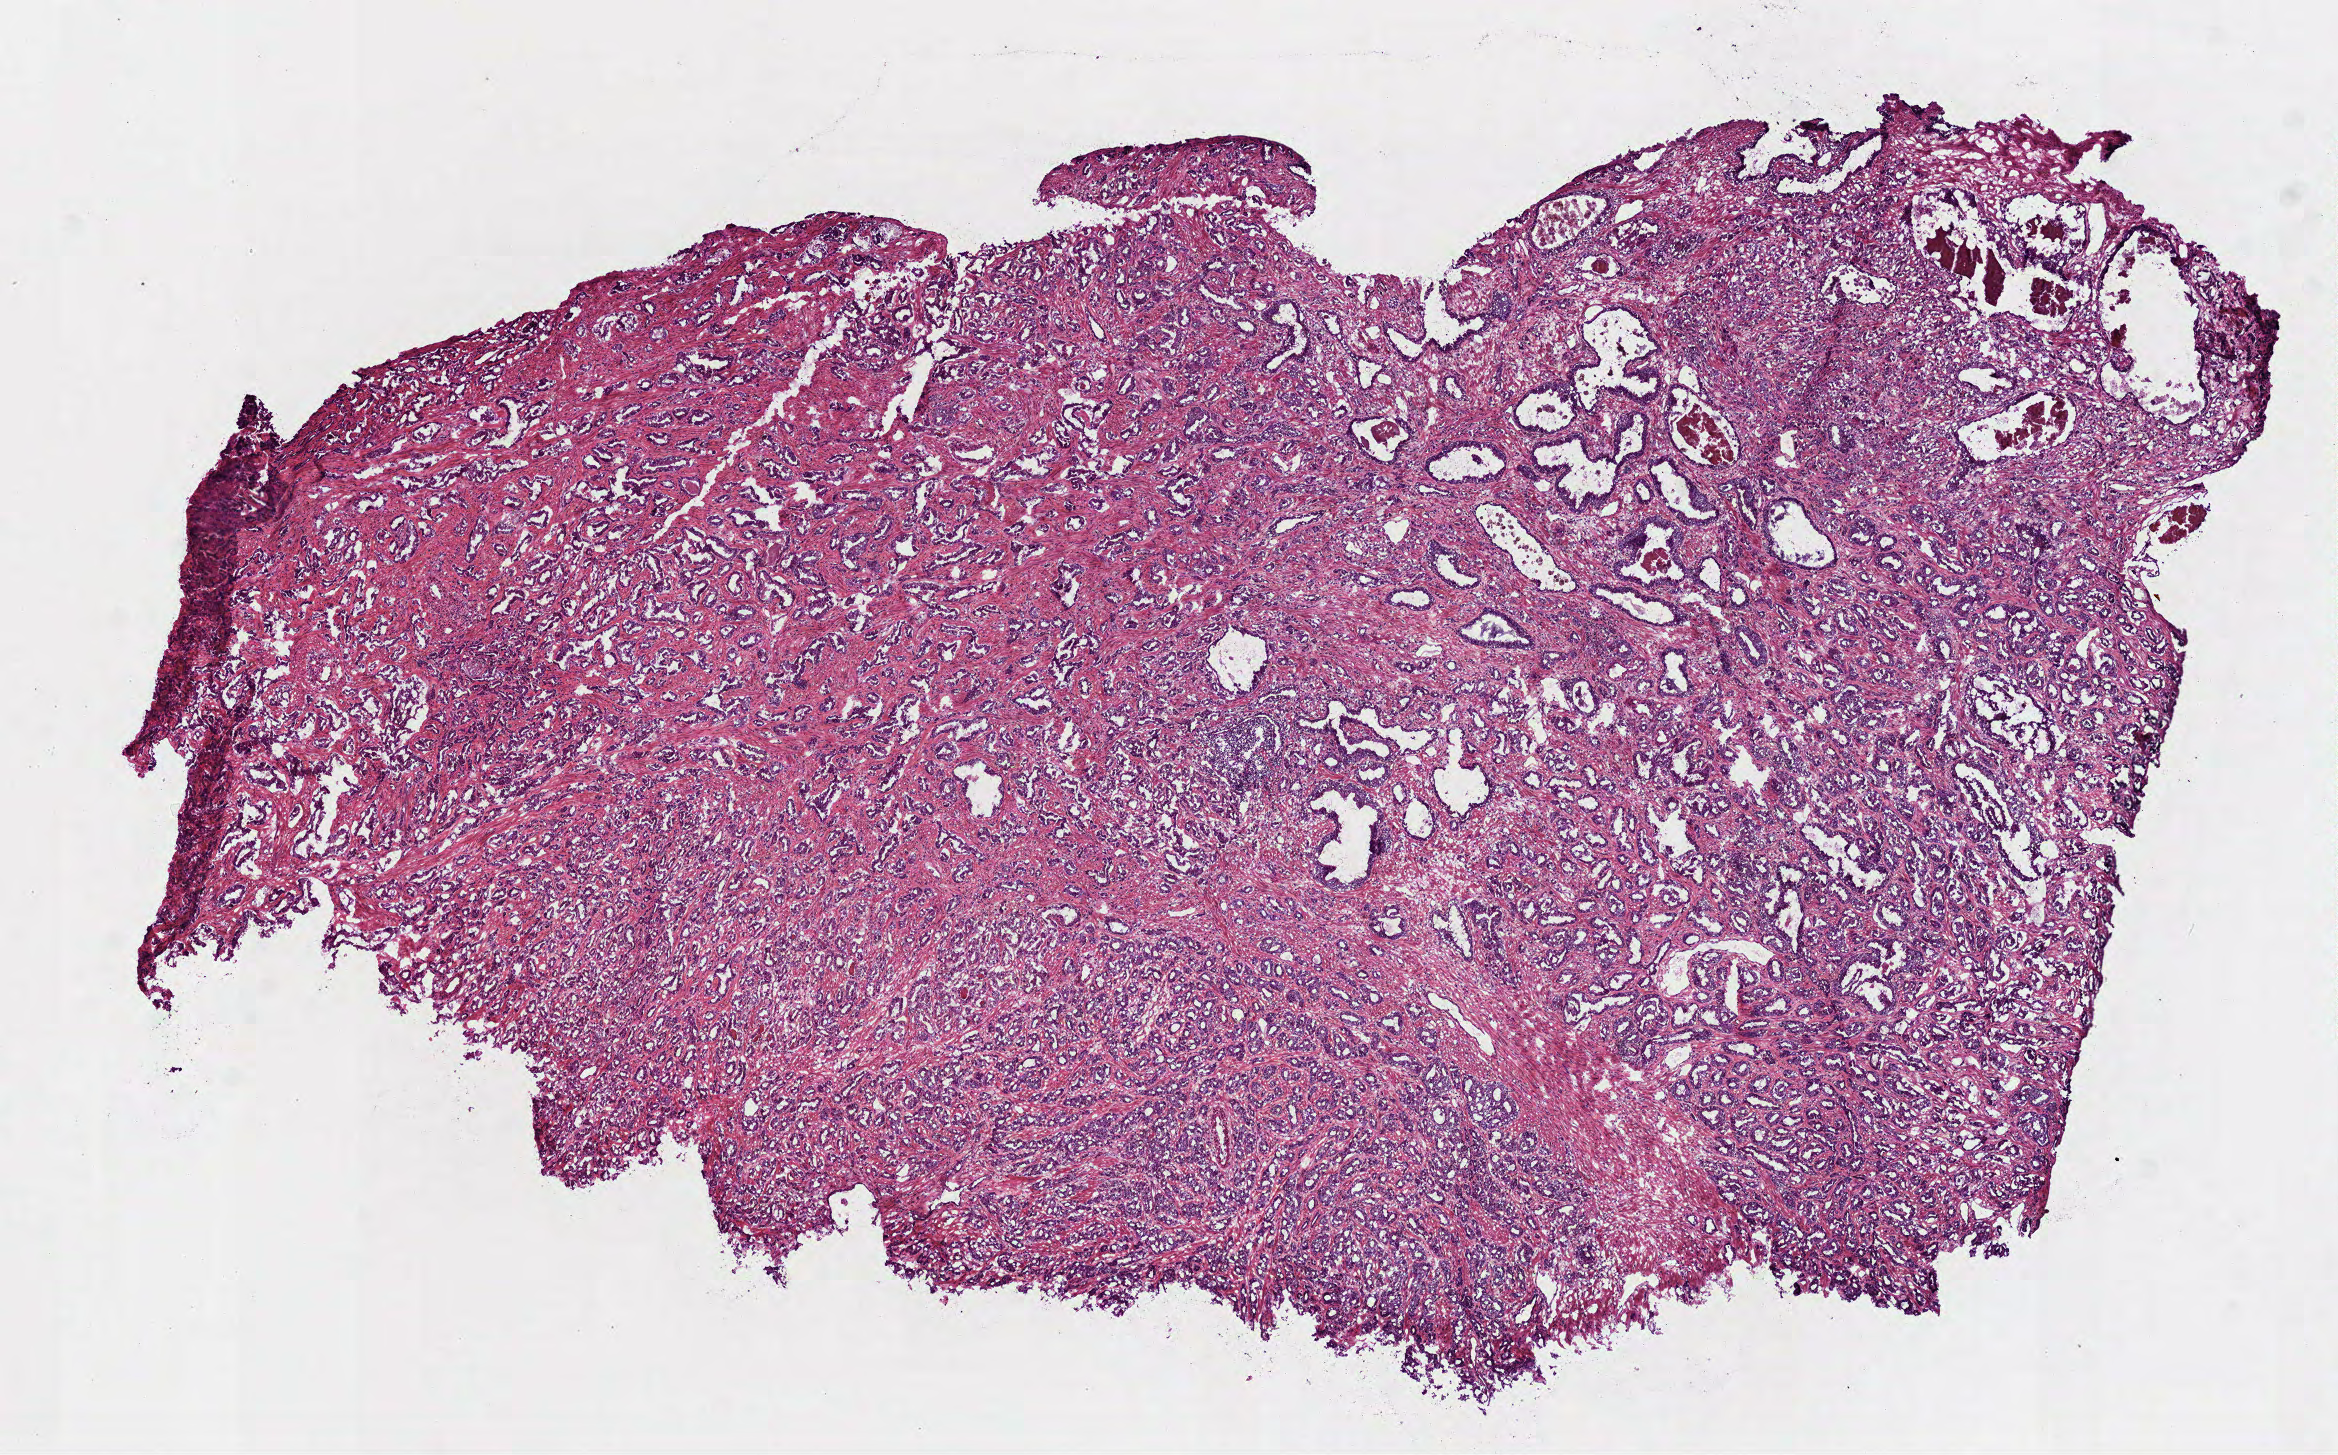
H&E whole-slide image — shown as a low-resolution overview of the whole scanned area (about 9.4 x 5.9 mm); frozen section; prostate, primary tumour sample. Male patient; age at initial diagnosis 69 years. Gleason score: 8 (4+4). Slide review estimates, as recorded: tumour cells 85%, tumour nuclei 85%, normal cells 7%, stromal cells 8%, necrosis 0%.
* lymph nodes positive (case pathology): 0 of 15 examined
* diagnosis: Acinar cell carcinoma (prostate gland)
* laterality: bilateral